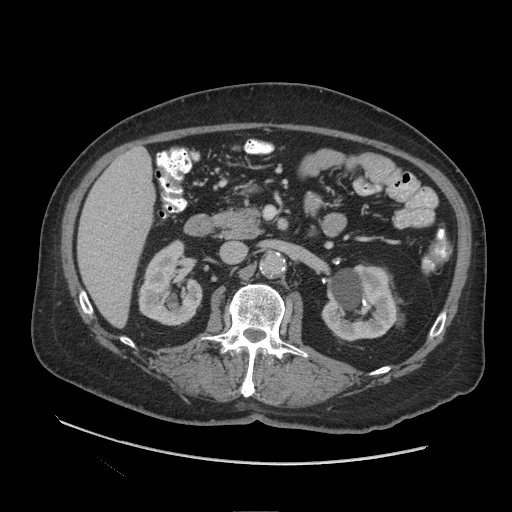
Contrast-enhanced abdominal CT (liver protocol), one axial slice; position 39 of 109 along the scan axis; 140 kVp; soft-tissue window (W 400 / L 40 HU); 512 × 512 image matrix. From the clinical record (not read from this slice): diagnosis: hepatocellular carcinoma (patient treated with transarterial chemoembolisation; whether this scan precedes or follows treatment is not stated here); TNM stage (as recorded): Stage-I; Child-Pugh class: A; tumour nodularity: uninodular.
Annotated regions visible in this slice (semi-automatic segmentation, software-assisted and operator-edited):
- liver parenchyma outside the tumour (the mass and vessels are separate outlines, so this box may not span the whole liver): box from (x=78, y=148) to (x=154, y=326) px